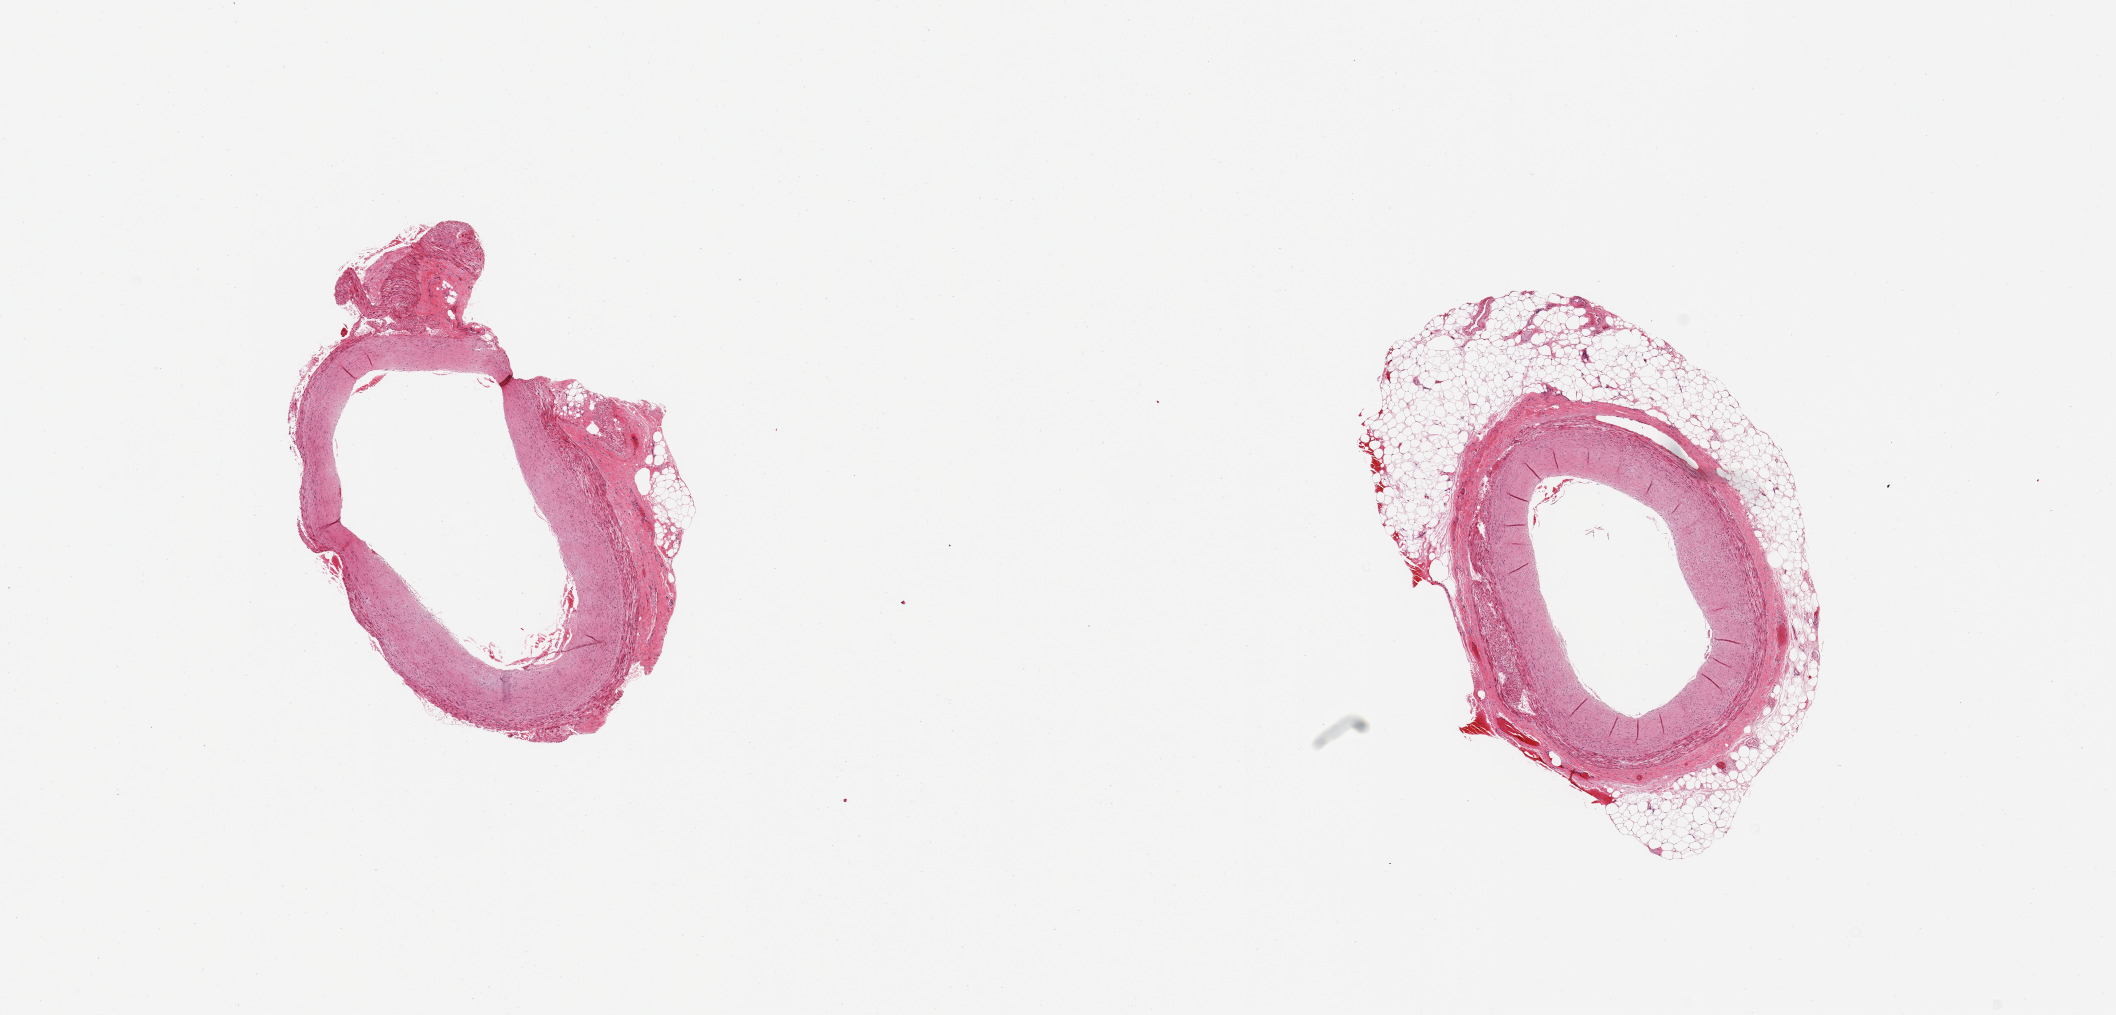
Hematoxylin and eosin (H&E) whole-slide image, whole scanned area (about 16.7 x 8.0 mm, slide scanned at 20x) shown as a low-resolution overview; PAXgene-fixed paraffin-embedded (PFPE) section; sampled site (target tissue): coronary artery; donor tissue sample. Donor sex: male.
Review note (as recorded): 2 pieces, minimal atherosis; adherent fat up to~ 1mm.